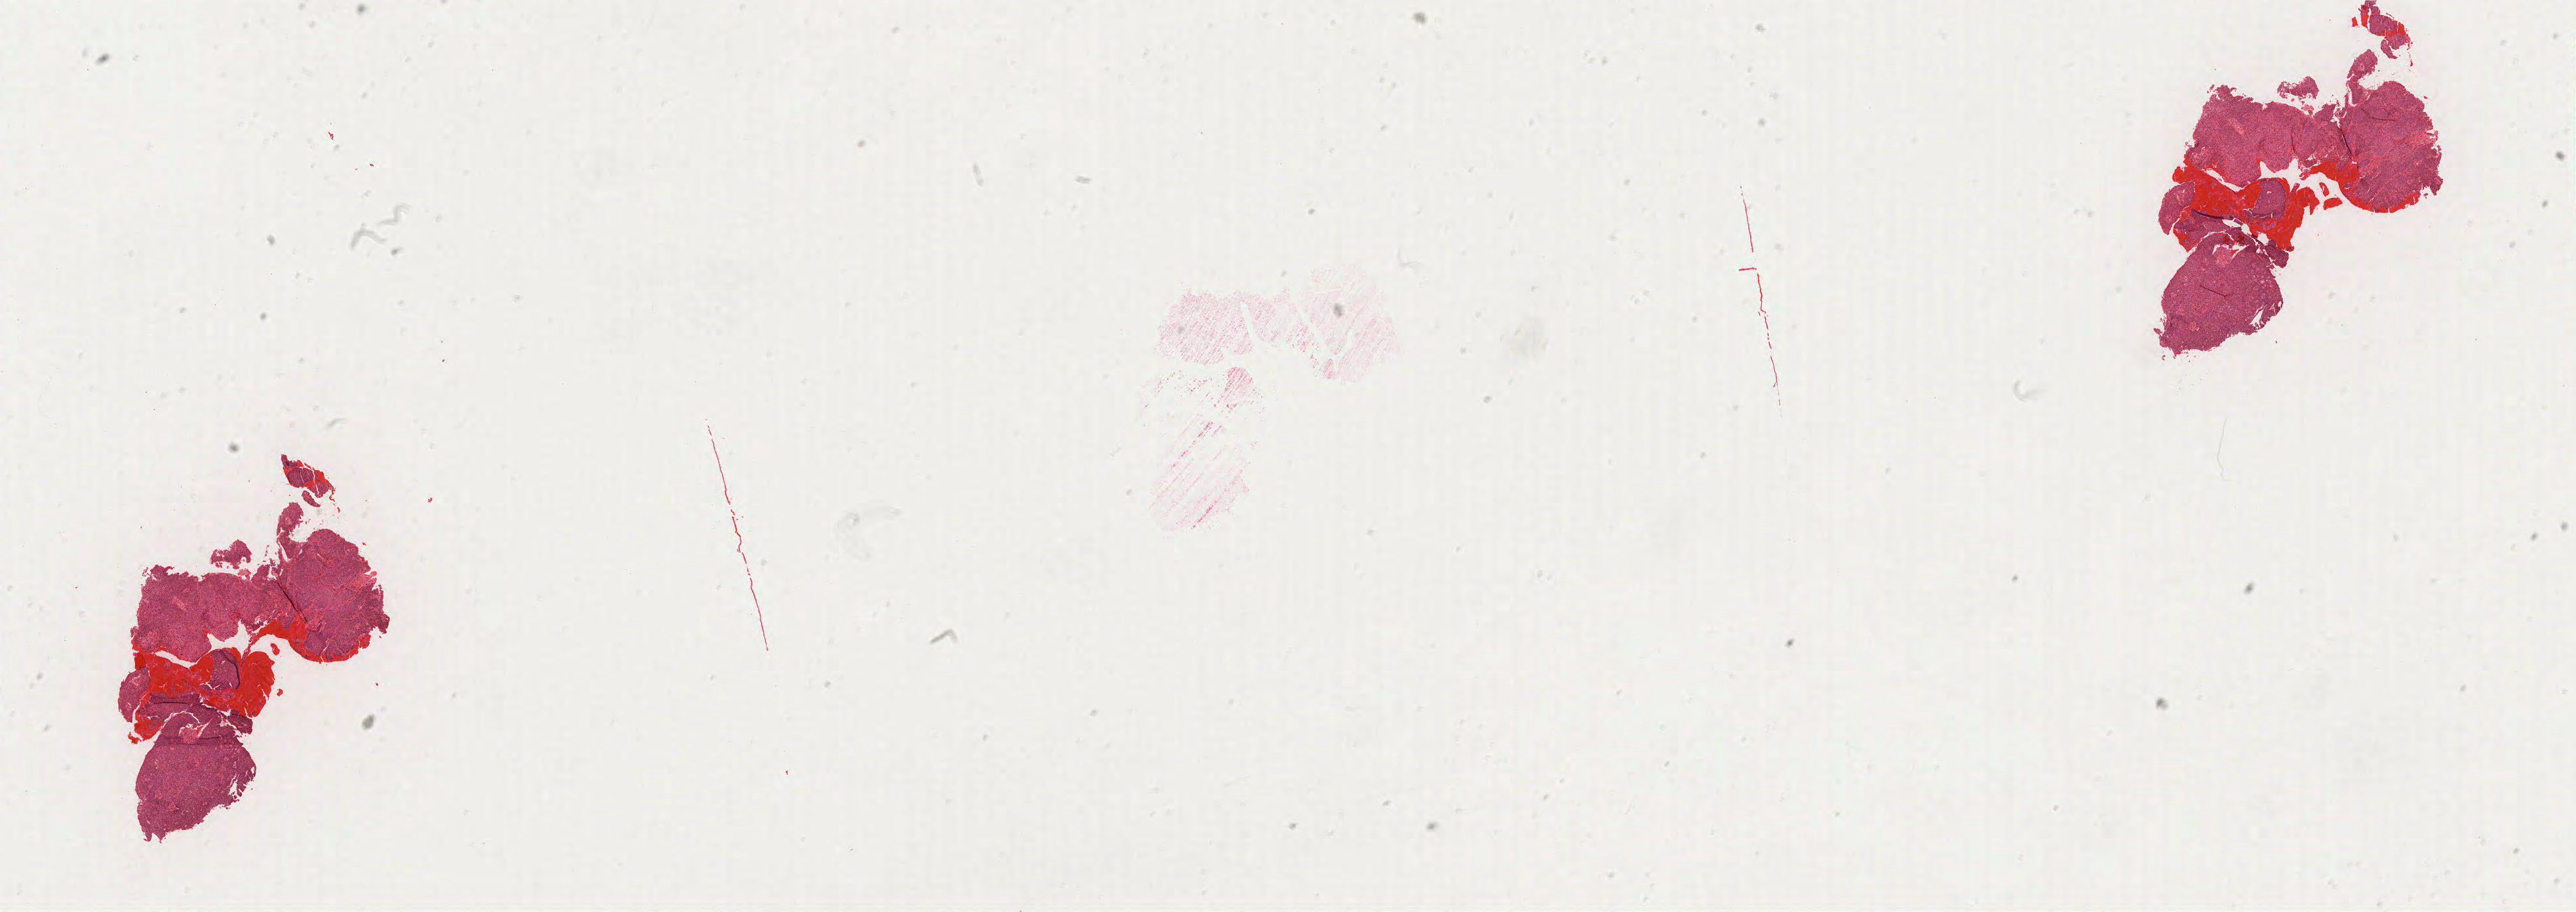
Whole-slide histology image, H&E — shown as a low-resolution overview of the whole scanned area (about 31.5 x 11.1 mm, slide scanned at 40x). Formalin-fixed paraffin-embedded (FFPE) diagnostic section. Sample: primary tumour, cervix. Patient: female, age at initial diagnosis 30 years. Histologic grade: G3 (poorly differentiated).
* histologic diagnosis: Squamous cell carcinoma, NOS (cervix uteri)